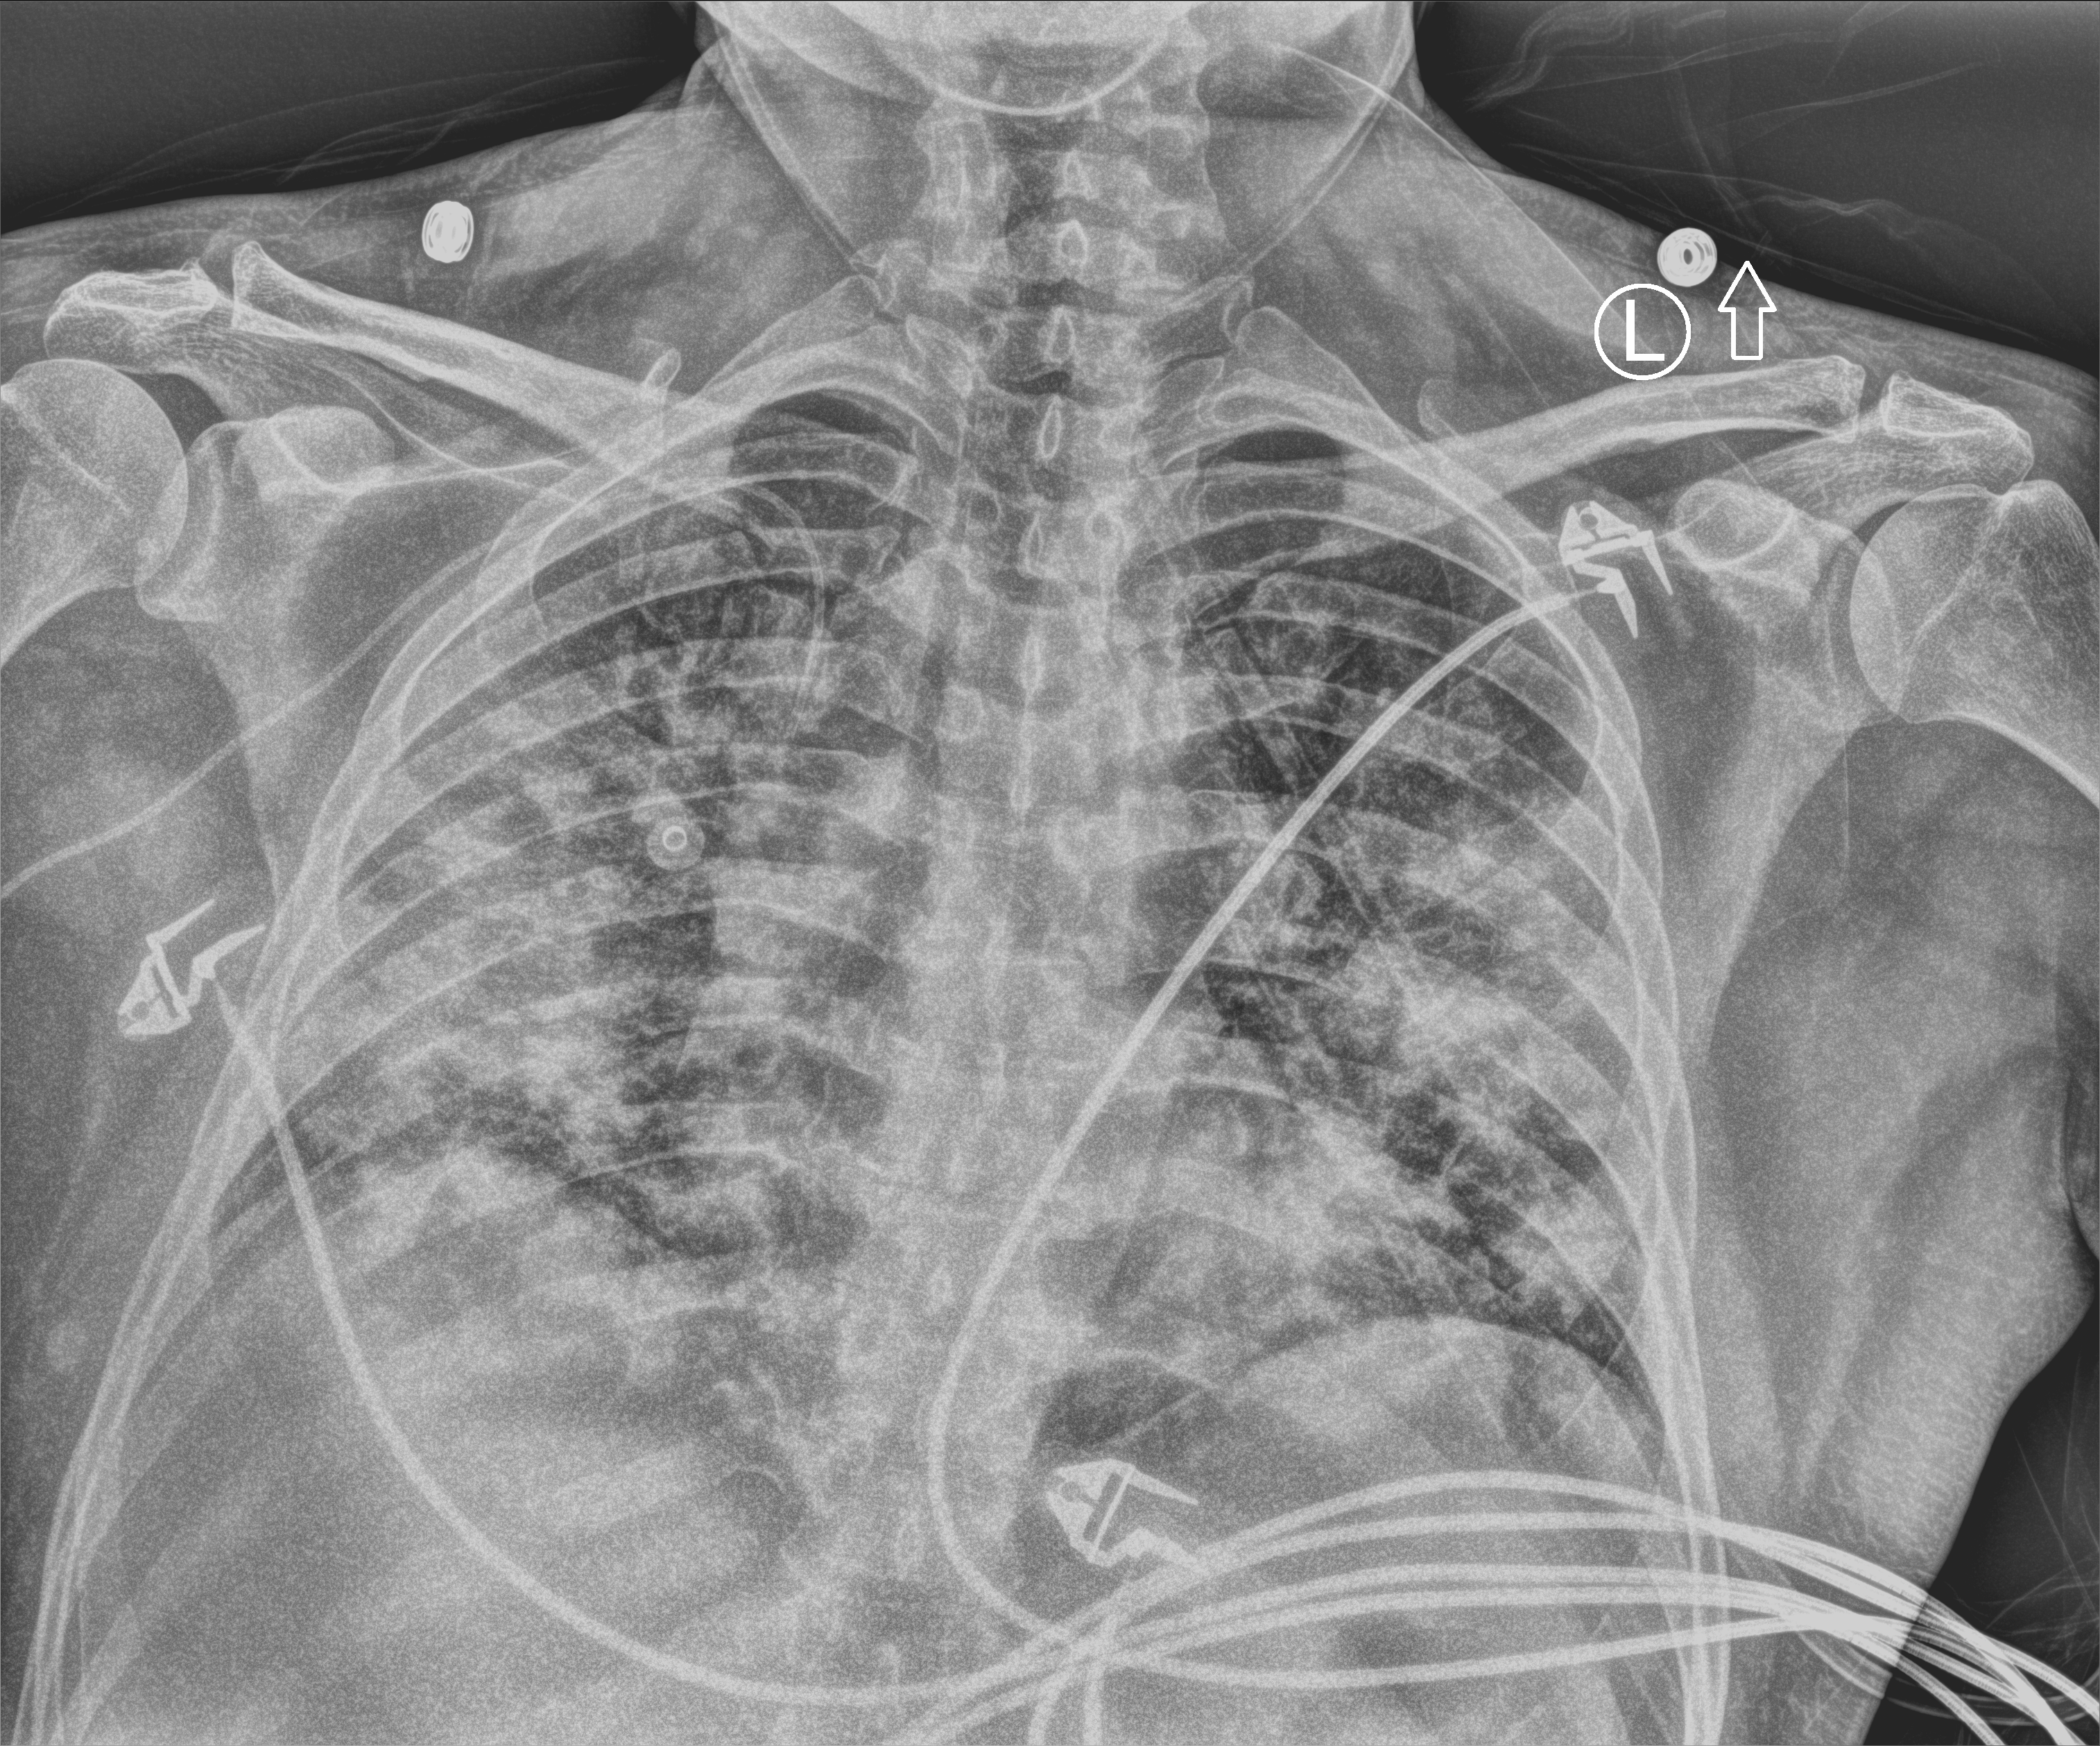
Chest X-ray (portable), anteroposterior (AP) projection. Patient hospitalised with COVID-19; male, aged 18–59 years.
From the hospital-stay record, not from the radiograph (when in the stay this image was taken is not recorded): length of hospital stay: 77 days; admitted to intensive care during this hospital stay: yes; hypertension (admission record): no.